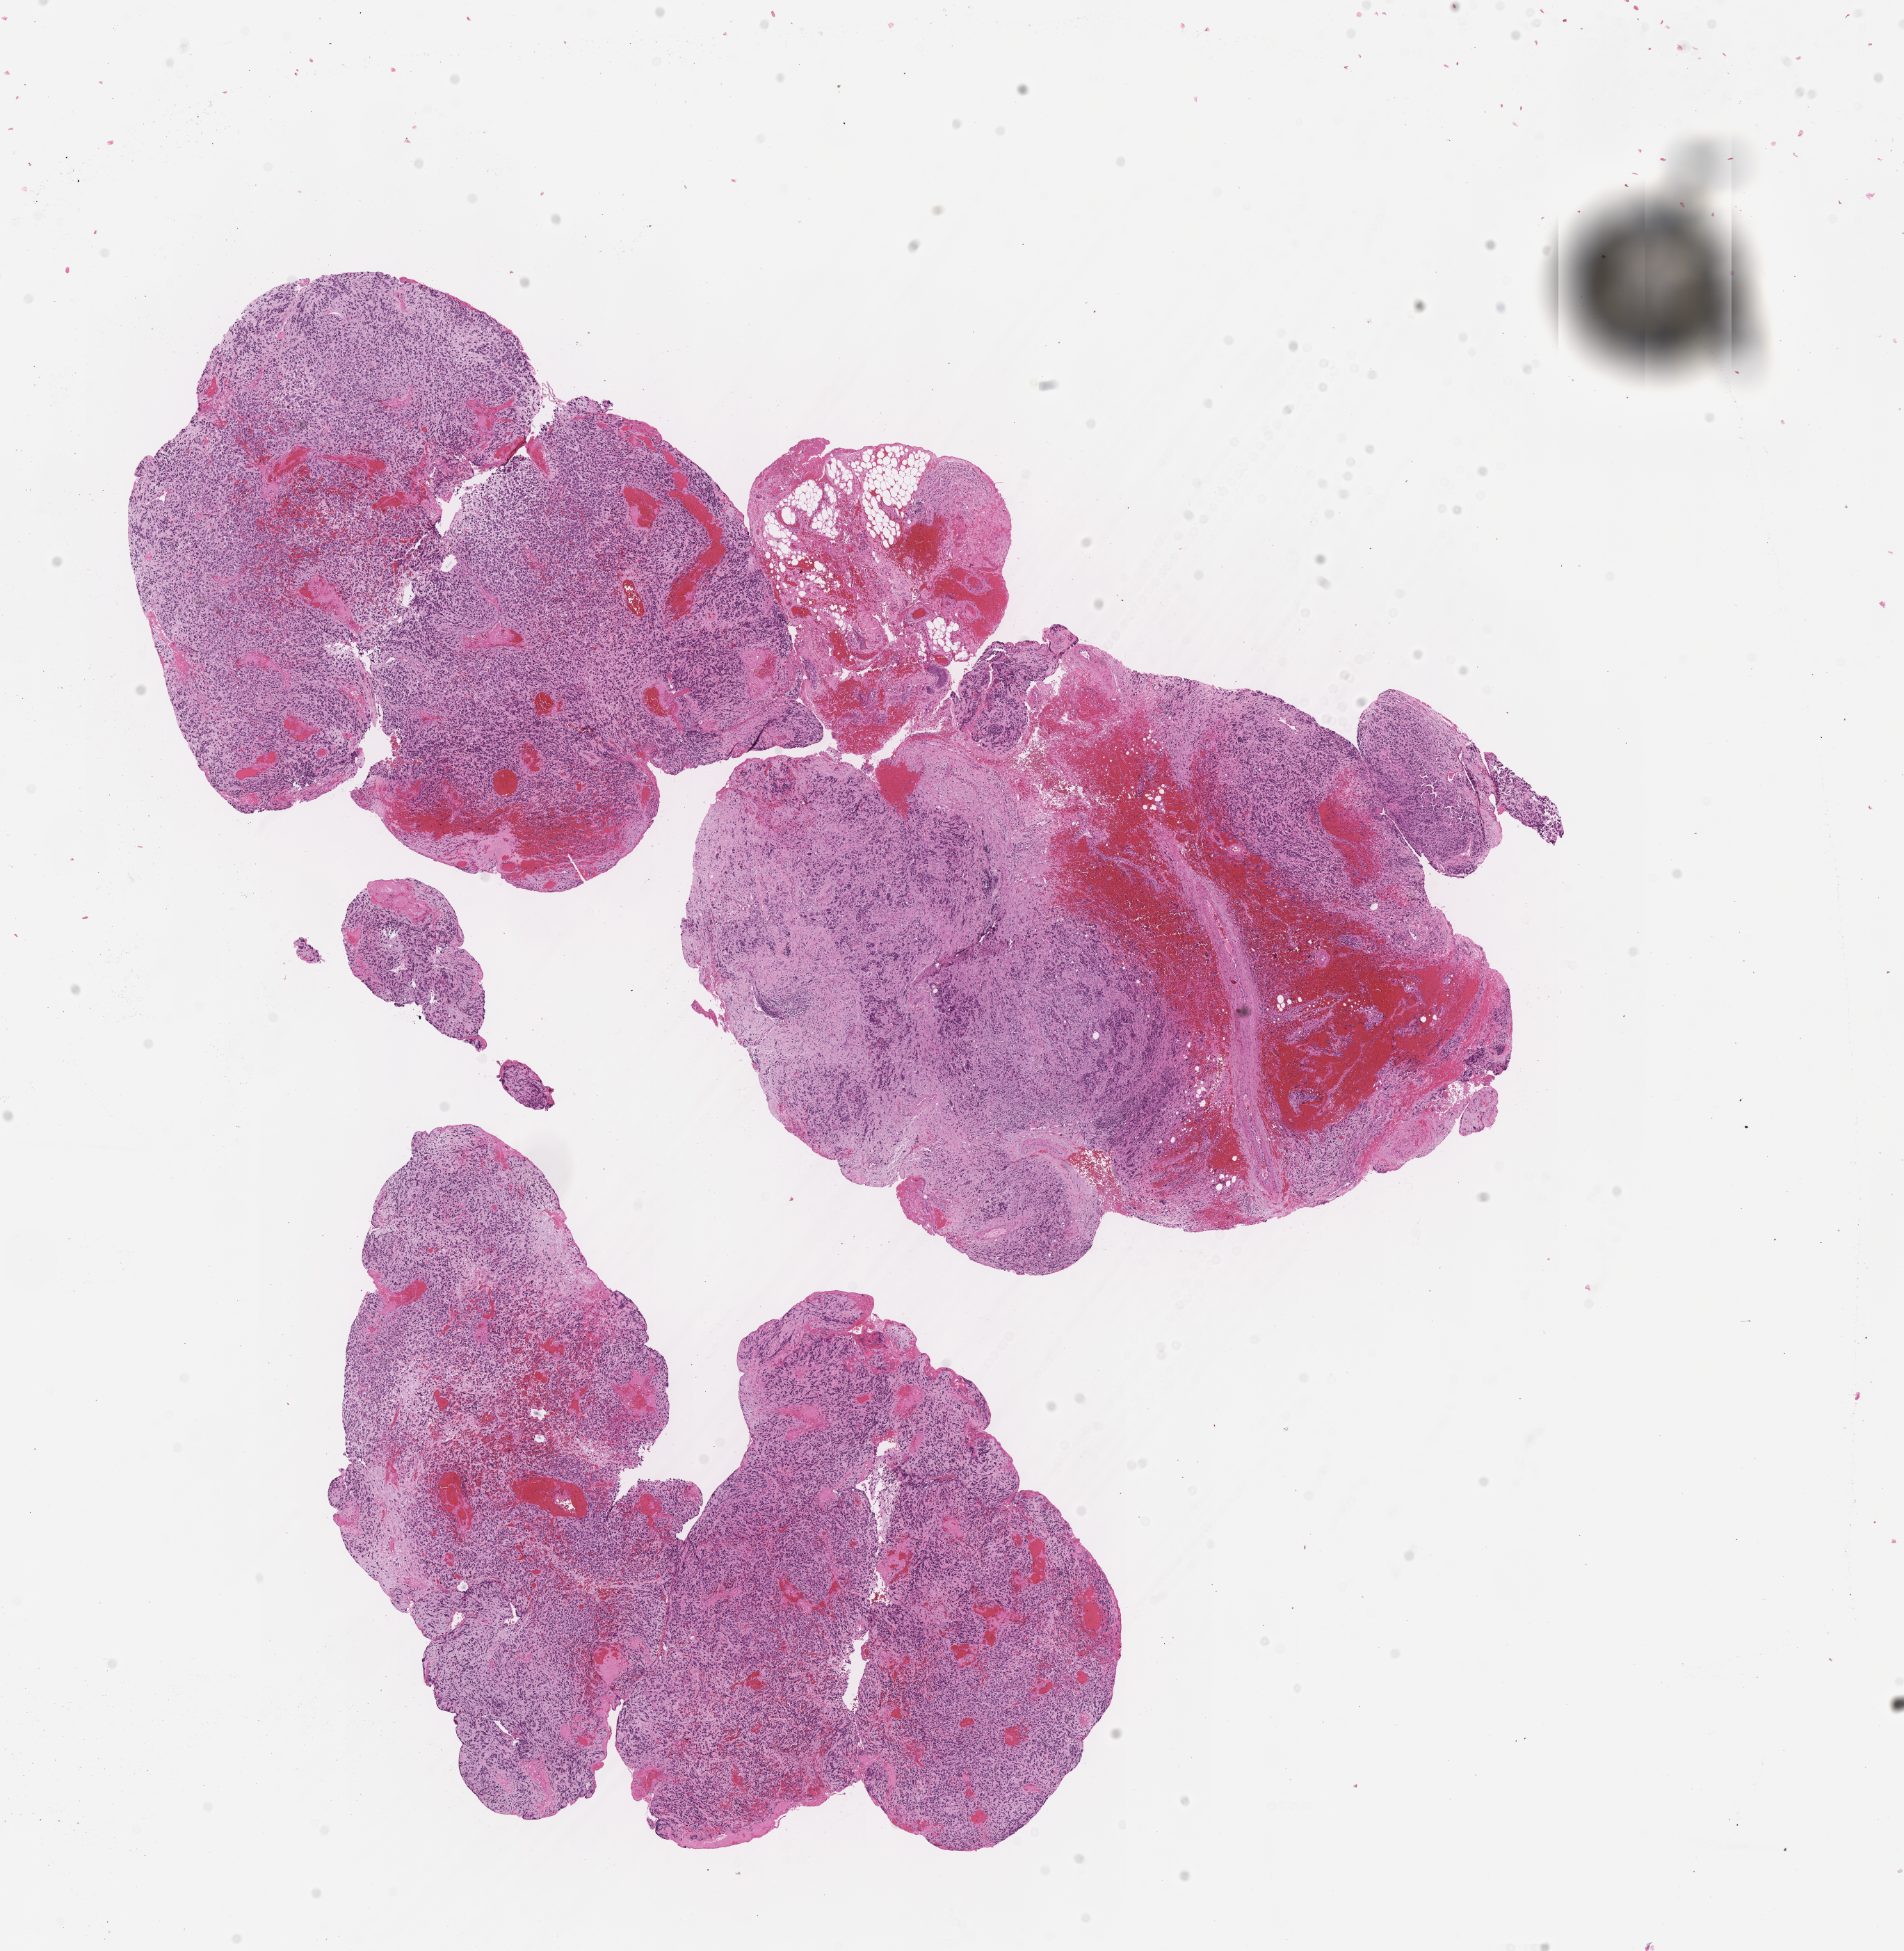
Whole-slide image, haematoxylin and eosin stain of tumor tissue — shown as a low-resolution overview of the whole scanned area (about 11.1 x 11.3 mm), FFPE section, sample anatomic site: eye, orbit-right medial. Female patient, age at diagnosis 3.2 years.
Stage (as recorded): 1. Metastatic status at presentation (as recorded): non-metastatic. Diagnosis: rhabdomyosarcoma; histological classification: embryonal rhabdomyosarcoma.